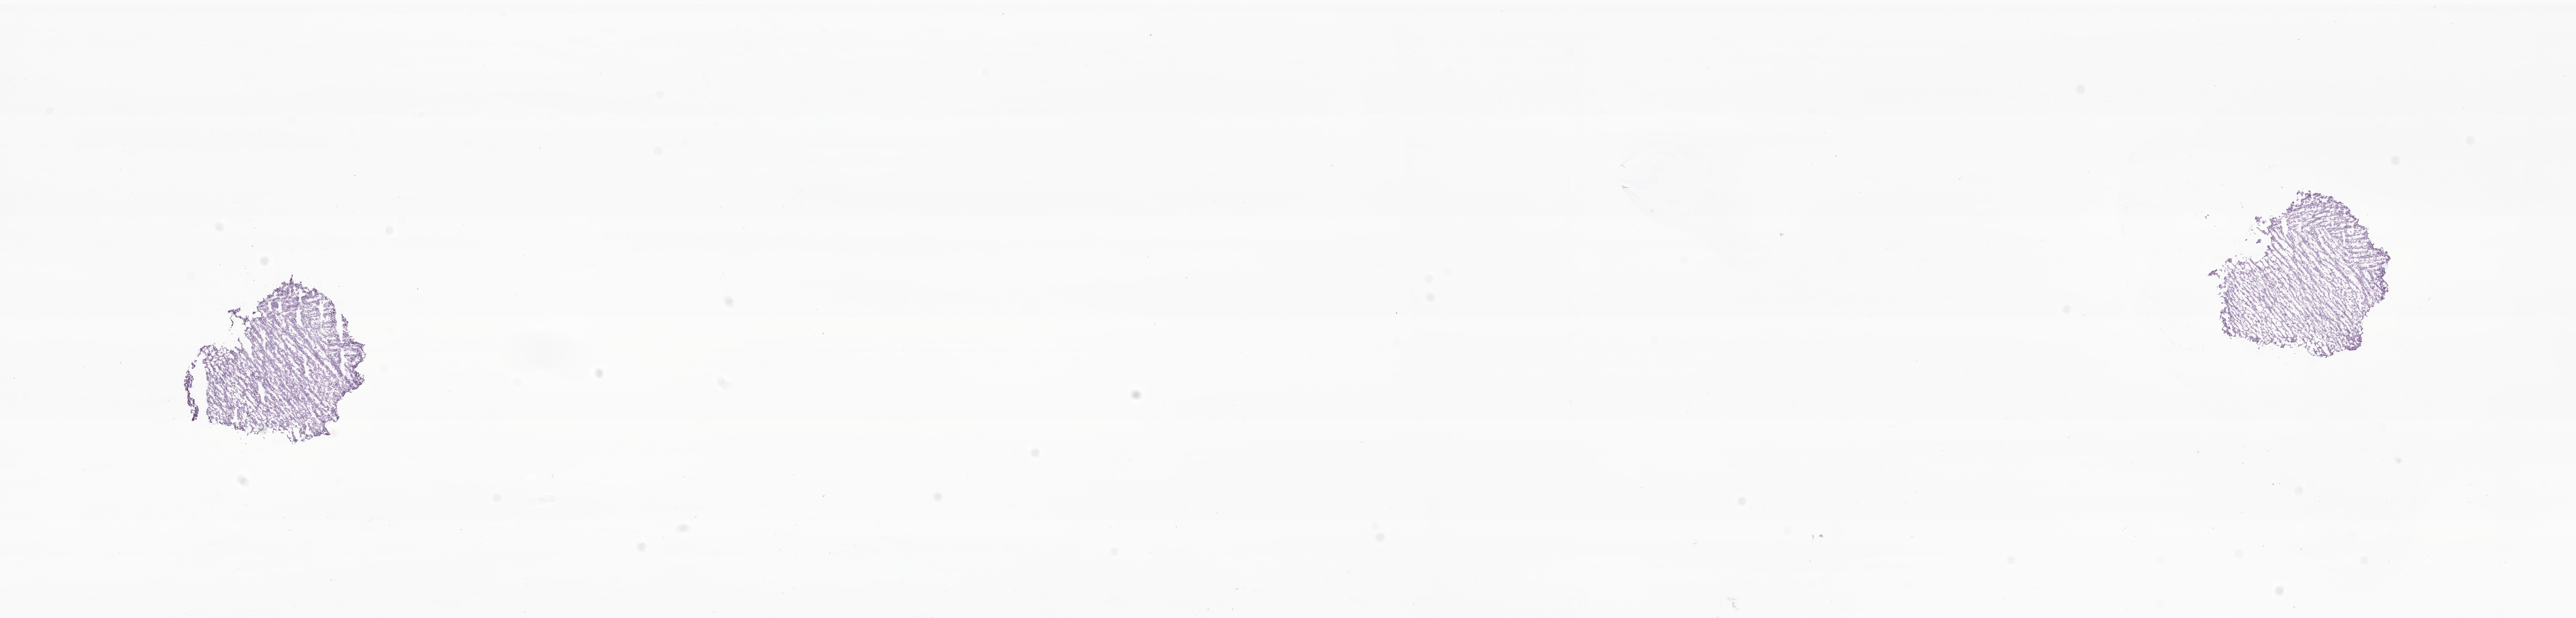
Digitized haematoxylin and eosin-stained section of tumor tissue from the brain — low-resolution overview of the scanned area, about 27.1 x 6.5 mm; cryosection (OCT / tissue freezing medium). Patient: male, age 106 months.
Diagnosis (ICD-O-3 morphology term): Neoplasm, malignant.